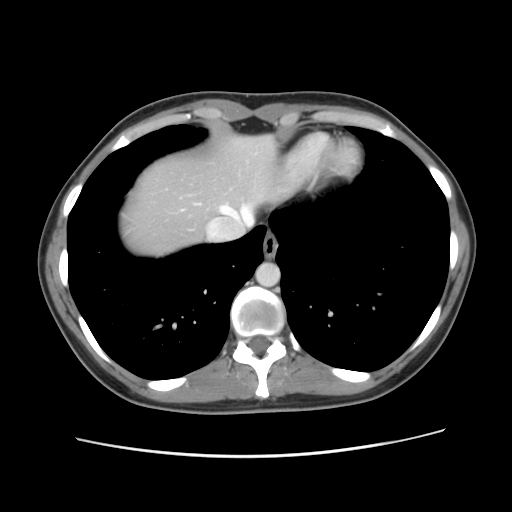
Contrast-enhanced abdominal CT, one axial slice. Intravenous contrast given. Soft-tissue window (W 400 / L 40 HU). 2.5 mm slice thickness. 512 × 512 image matrix. Female patient, age 33 years. From the clinical record (not read from this slice): diagnosis: colorectal cancer liver metastases, imaged before liver resection; multiple liver metastases: yes; largest metastasis: 4.5 cm; chemotherapy before resection: no.
Outlined on this slice (expert manual segmentation):
- hepatic veins: box from (x=220, y=204) to (x=254, y=225) px
- liver: (x=120, y=135)–(x=298, y=256)
- planned liver remnant (the part of the liver to remain after resection): (x=120, y=135)–(x=298, y=256)